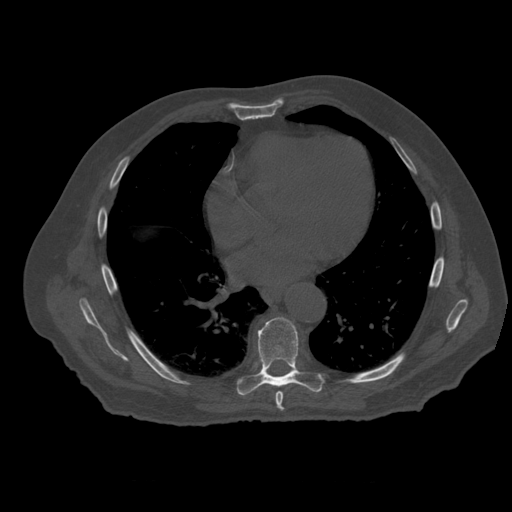
CT including the spine, one axial slice. Slice 345 of 399 in the series (ordered by position). 120 kVp. Bone window (W 1800 / L 400 HU). 1.25 mm slice thickness. 512 × 512 image matrix, field of view 407 × 407 mm. Patient age 73 years. Case-level facts recorded for this patient, not image findings: primary cancer: prostate.
Outlined on this slice (semi-automatically segmented with operator editing):
- T7 vertebra: bounding box <276,392,284,412> (left, top, right, bottom; pixels)
- T8 vertebra: <237,317,325,396>